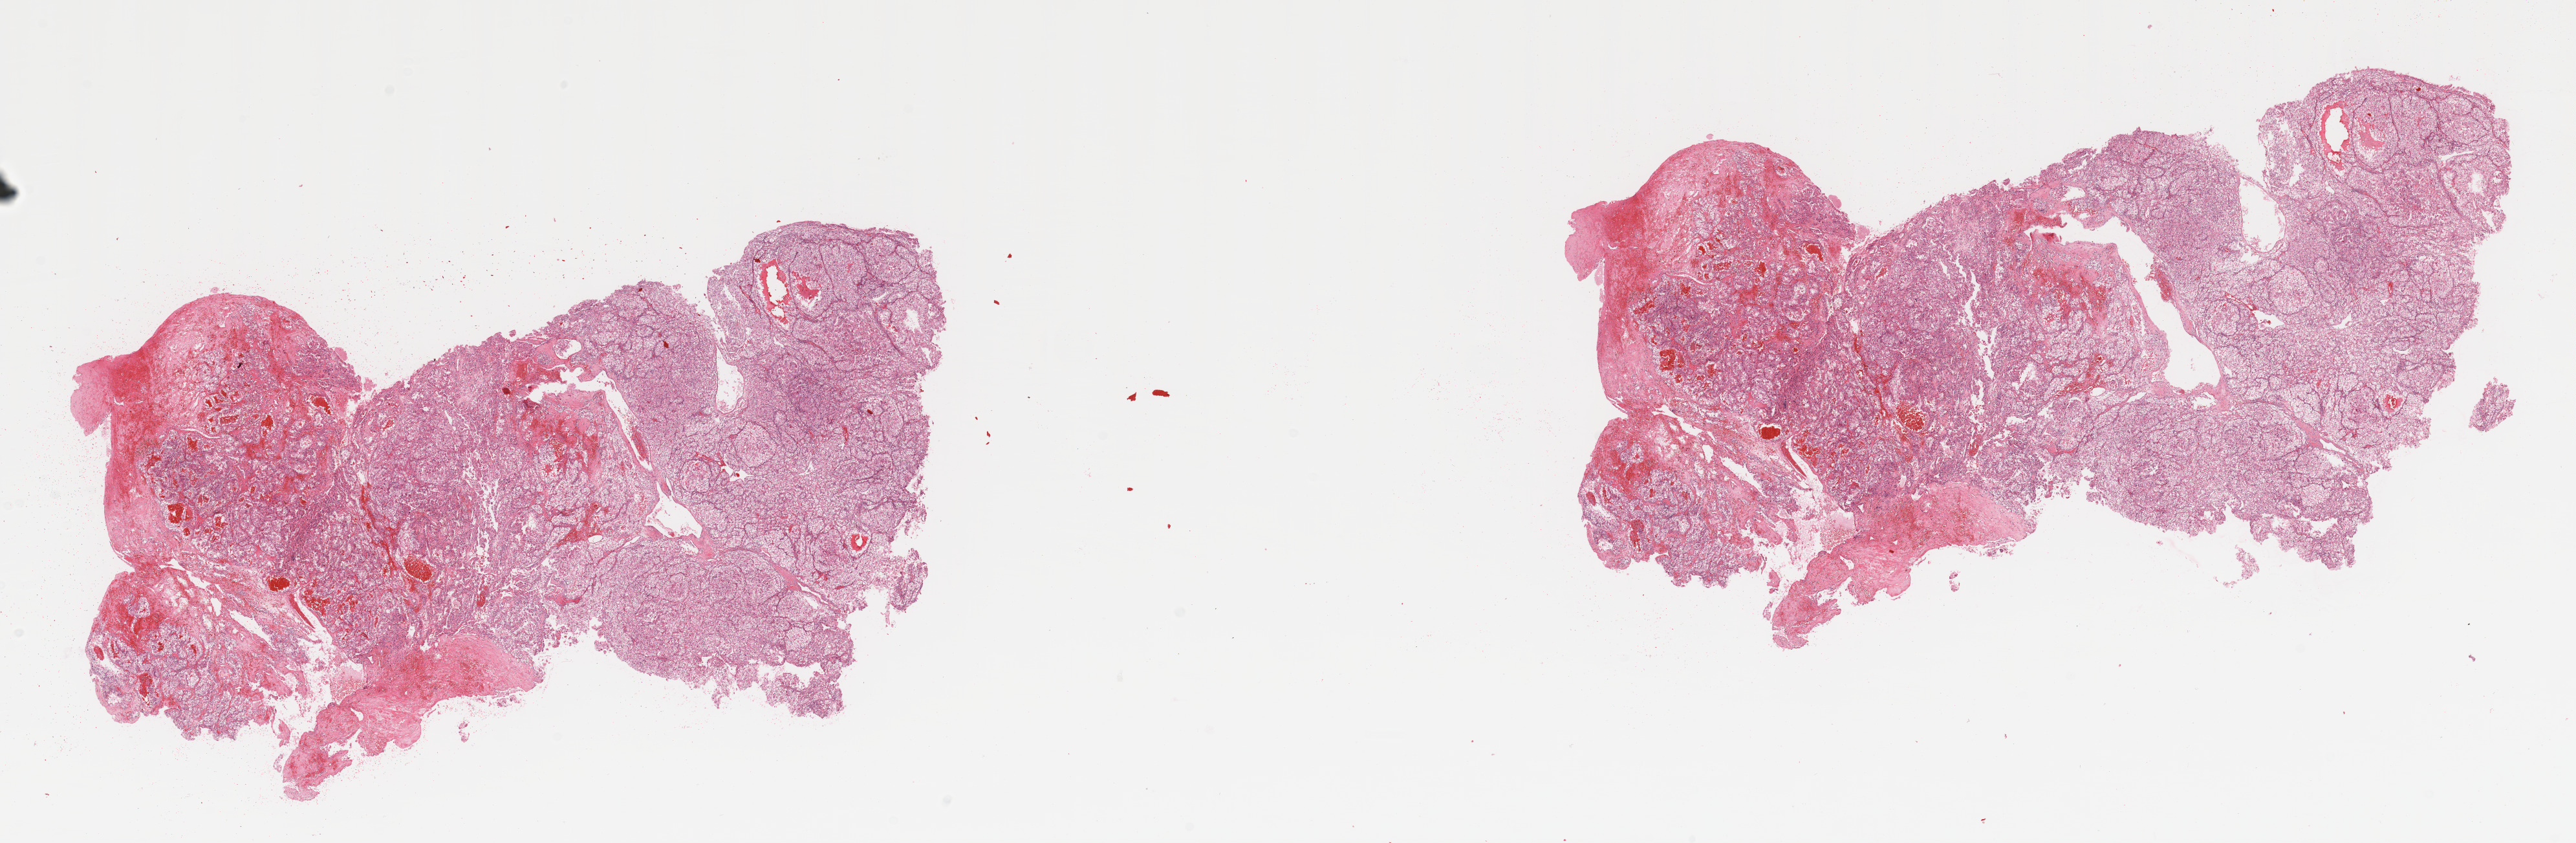
Whole-slide histology image, H&E, low-resolution overview of the scanned area, about 31.5 x 10.3 mm (acquisition: 20x scan); tumour tissue sample, sampled site: kidney. 74-year-old male patient. Histologic grade: G3 (poorly differentiated). Composition of this section per pathologist review: tumour nuclei 85%, necrosis 5%.
AJCC pathologic stage: I. Diagnosis: Renal cell carcinoma, NOS. Primary tumour site (as recorded): lower pole.